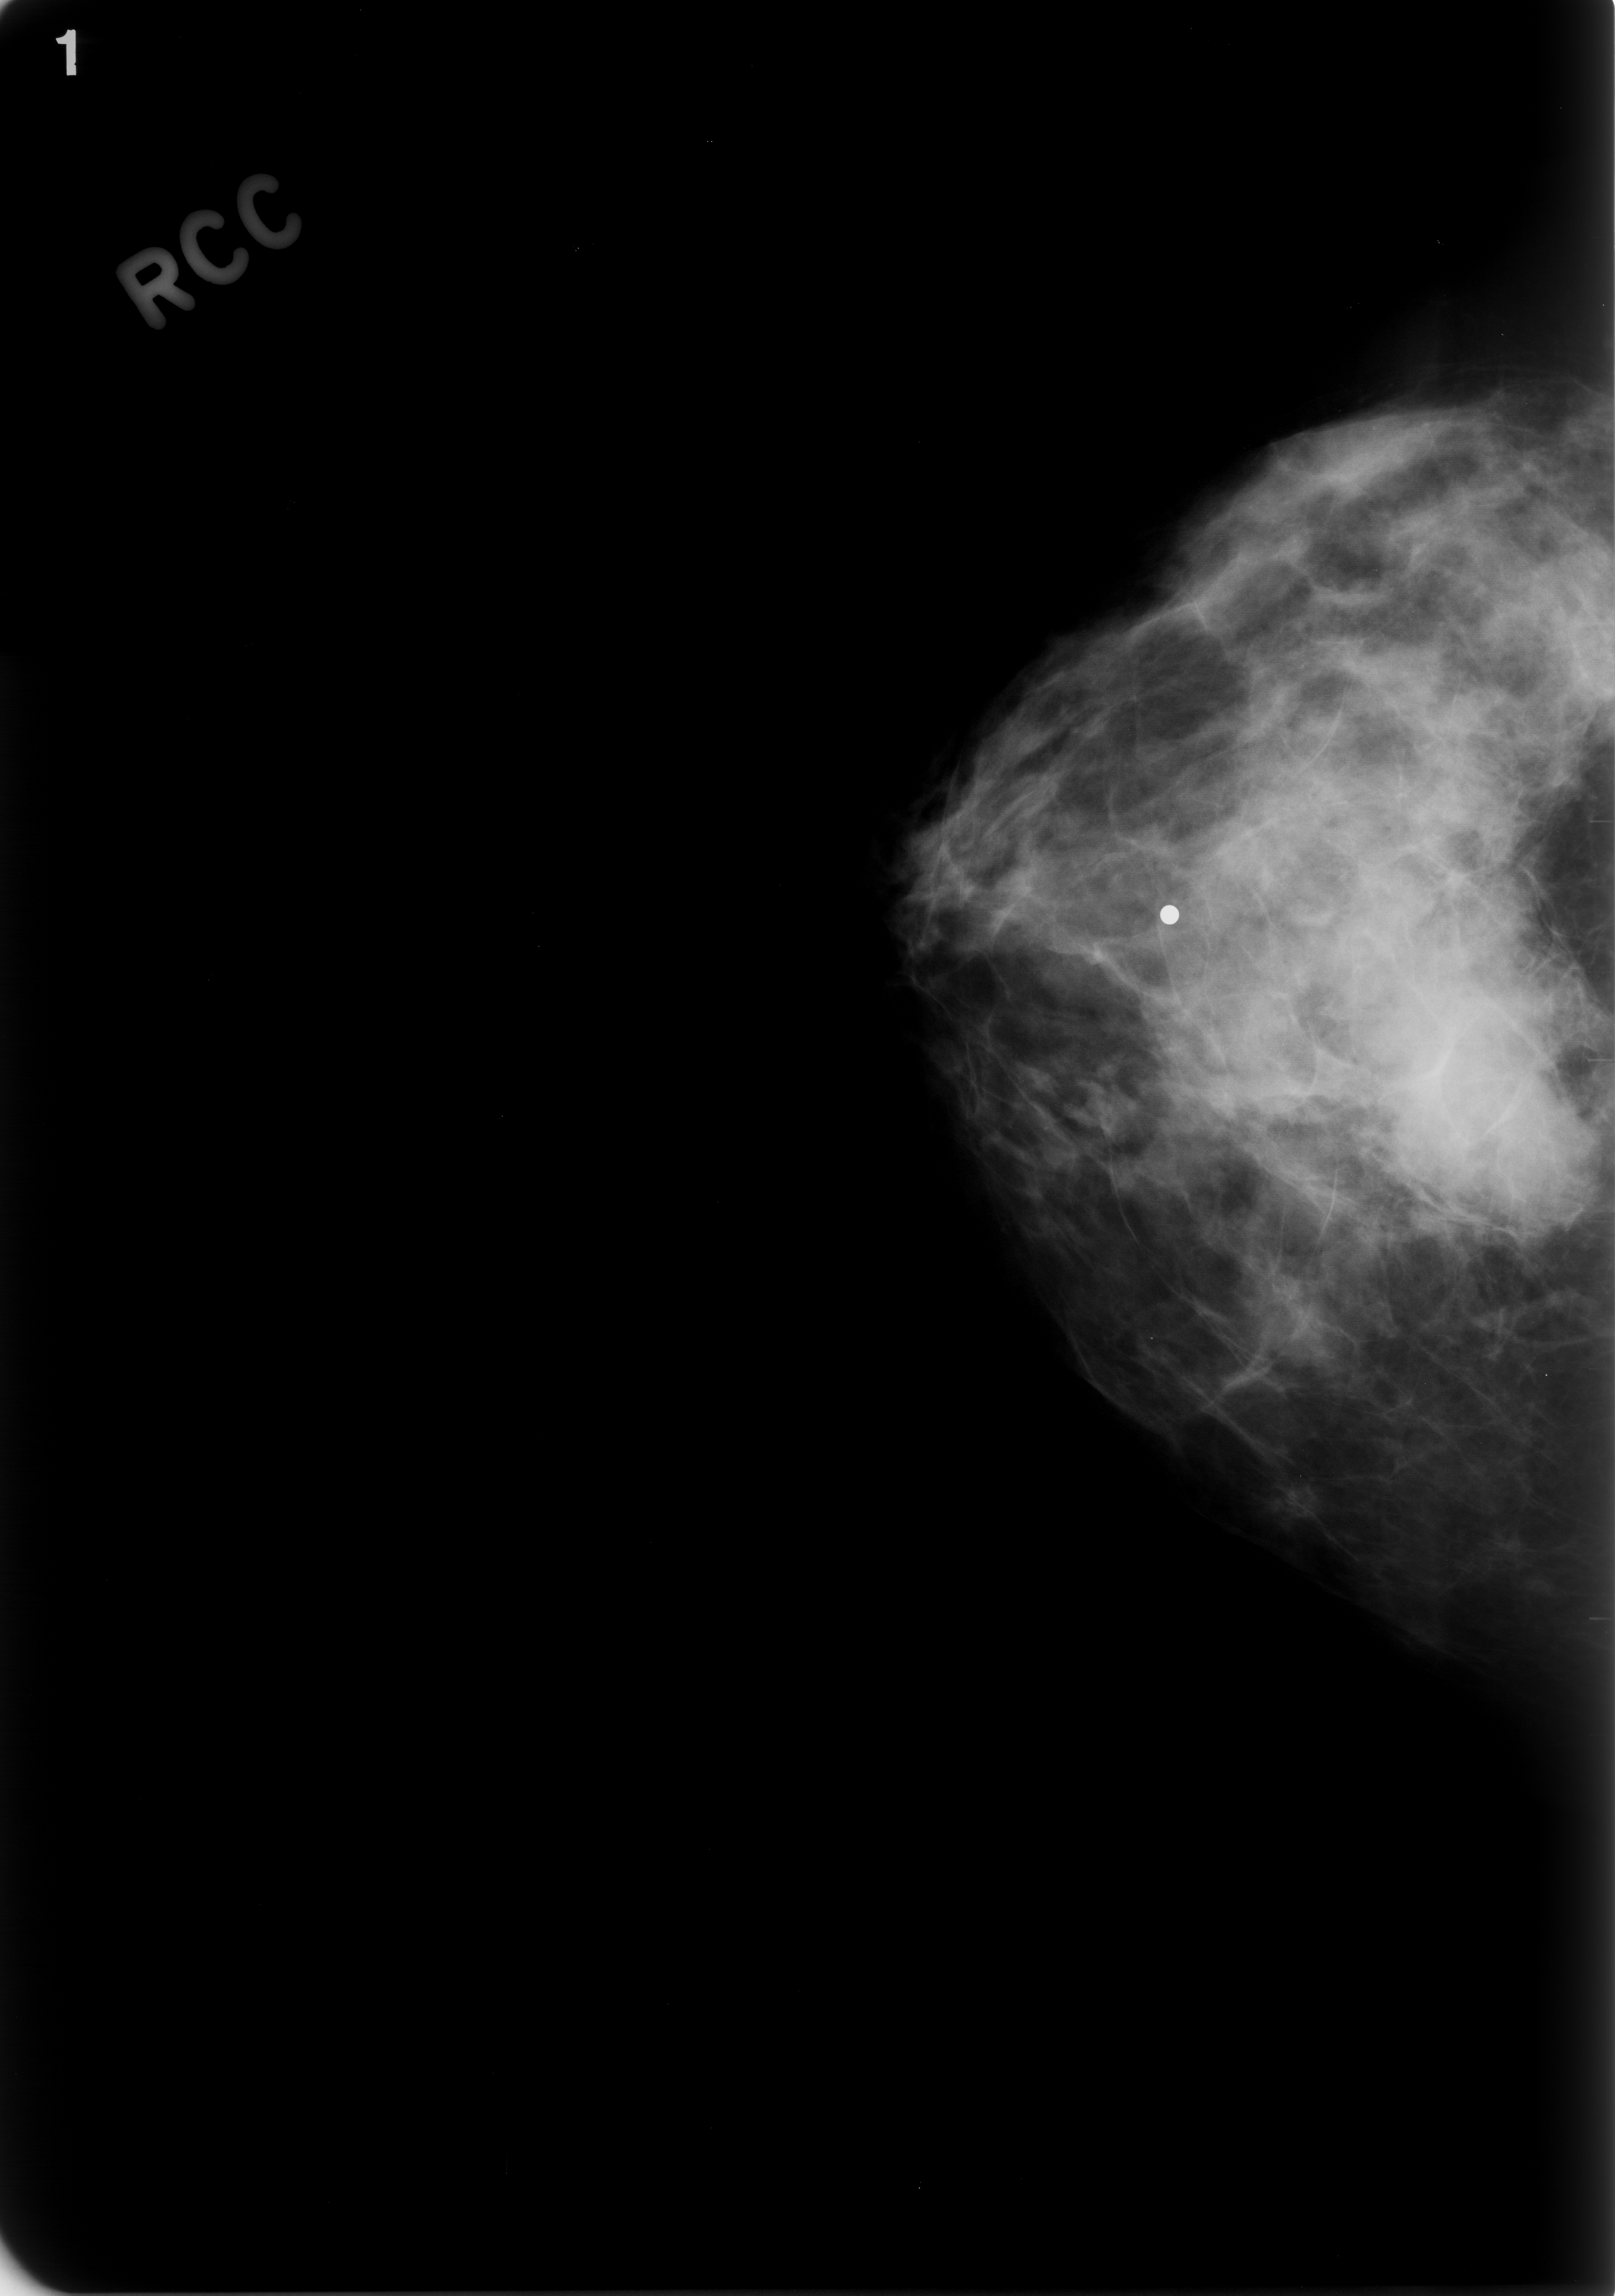
Mammogram (digitized film); right breast; craniocaudal (CC) view; BI-RADS breast density category 2 (scale 1–4); 1615 × 2296 image matrix.
Expert-marked regions of interest on this image (one box per marked abnormality):
- mass, shape asymmetric breast tissue, margins ill defined; BI-RADS assessment category 5; pathology result (as recorded, not read from the image): malignant: box from (x=1132, y=692) to (x=1574, y=1180) px